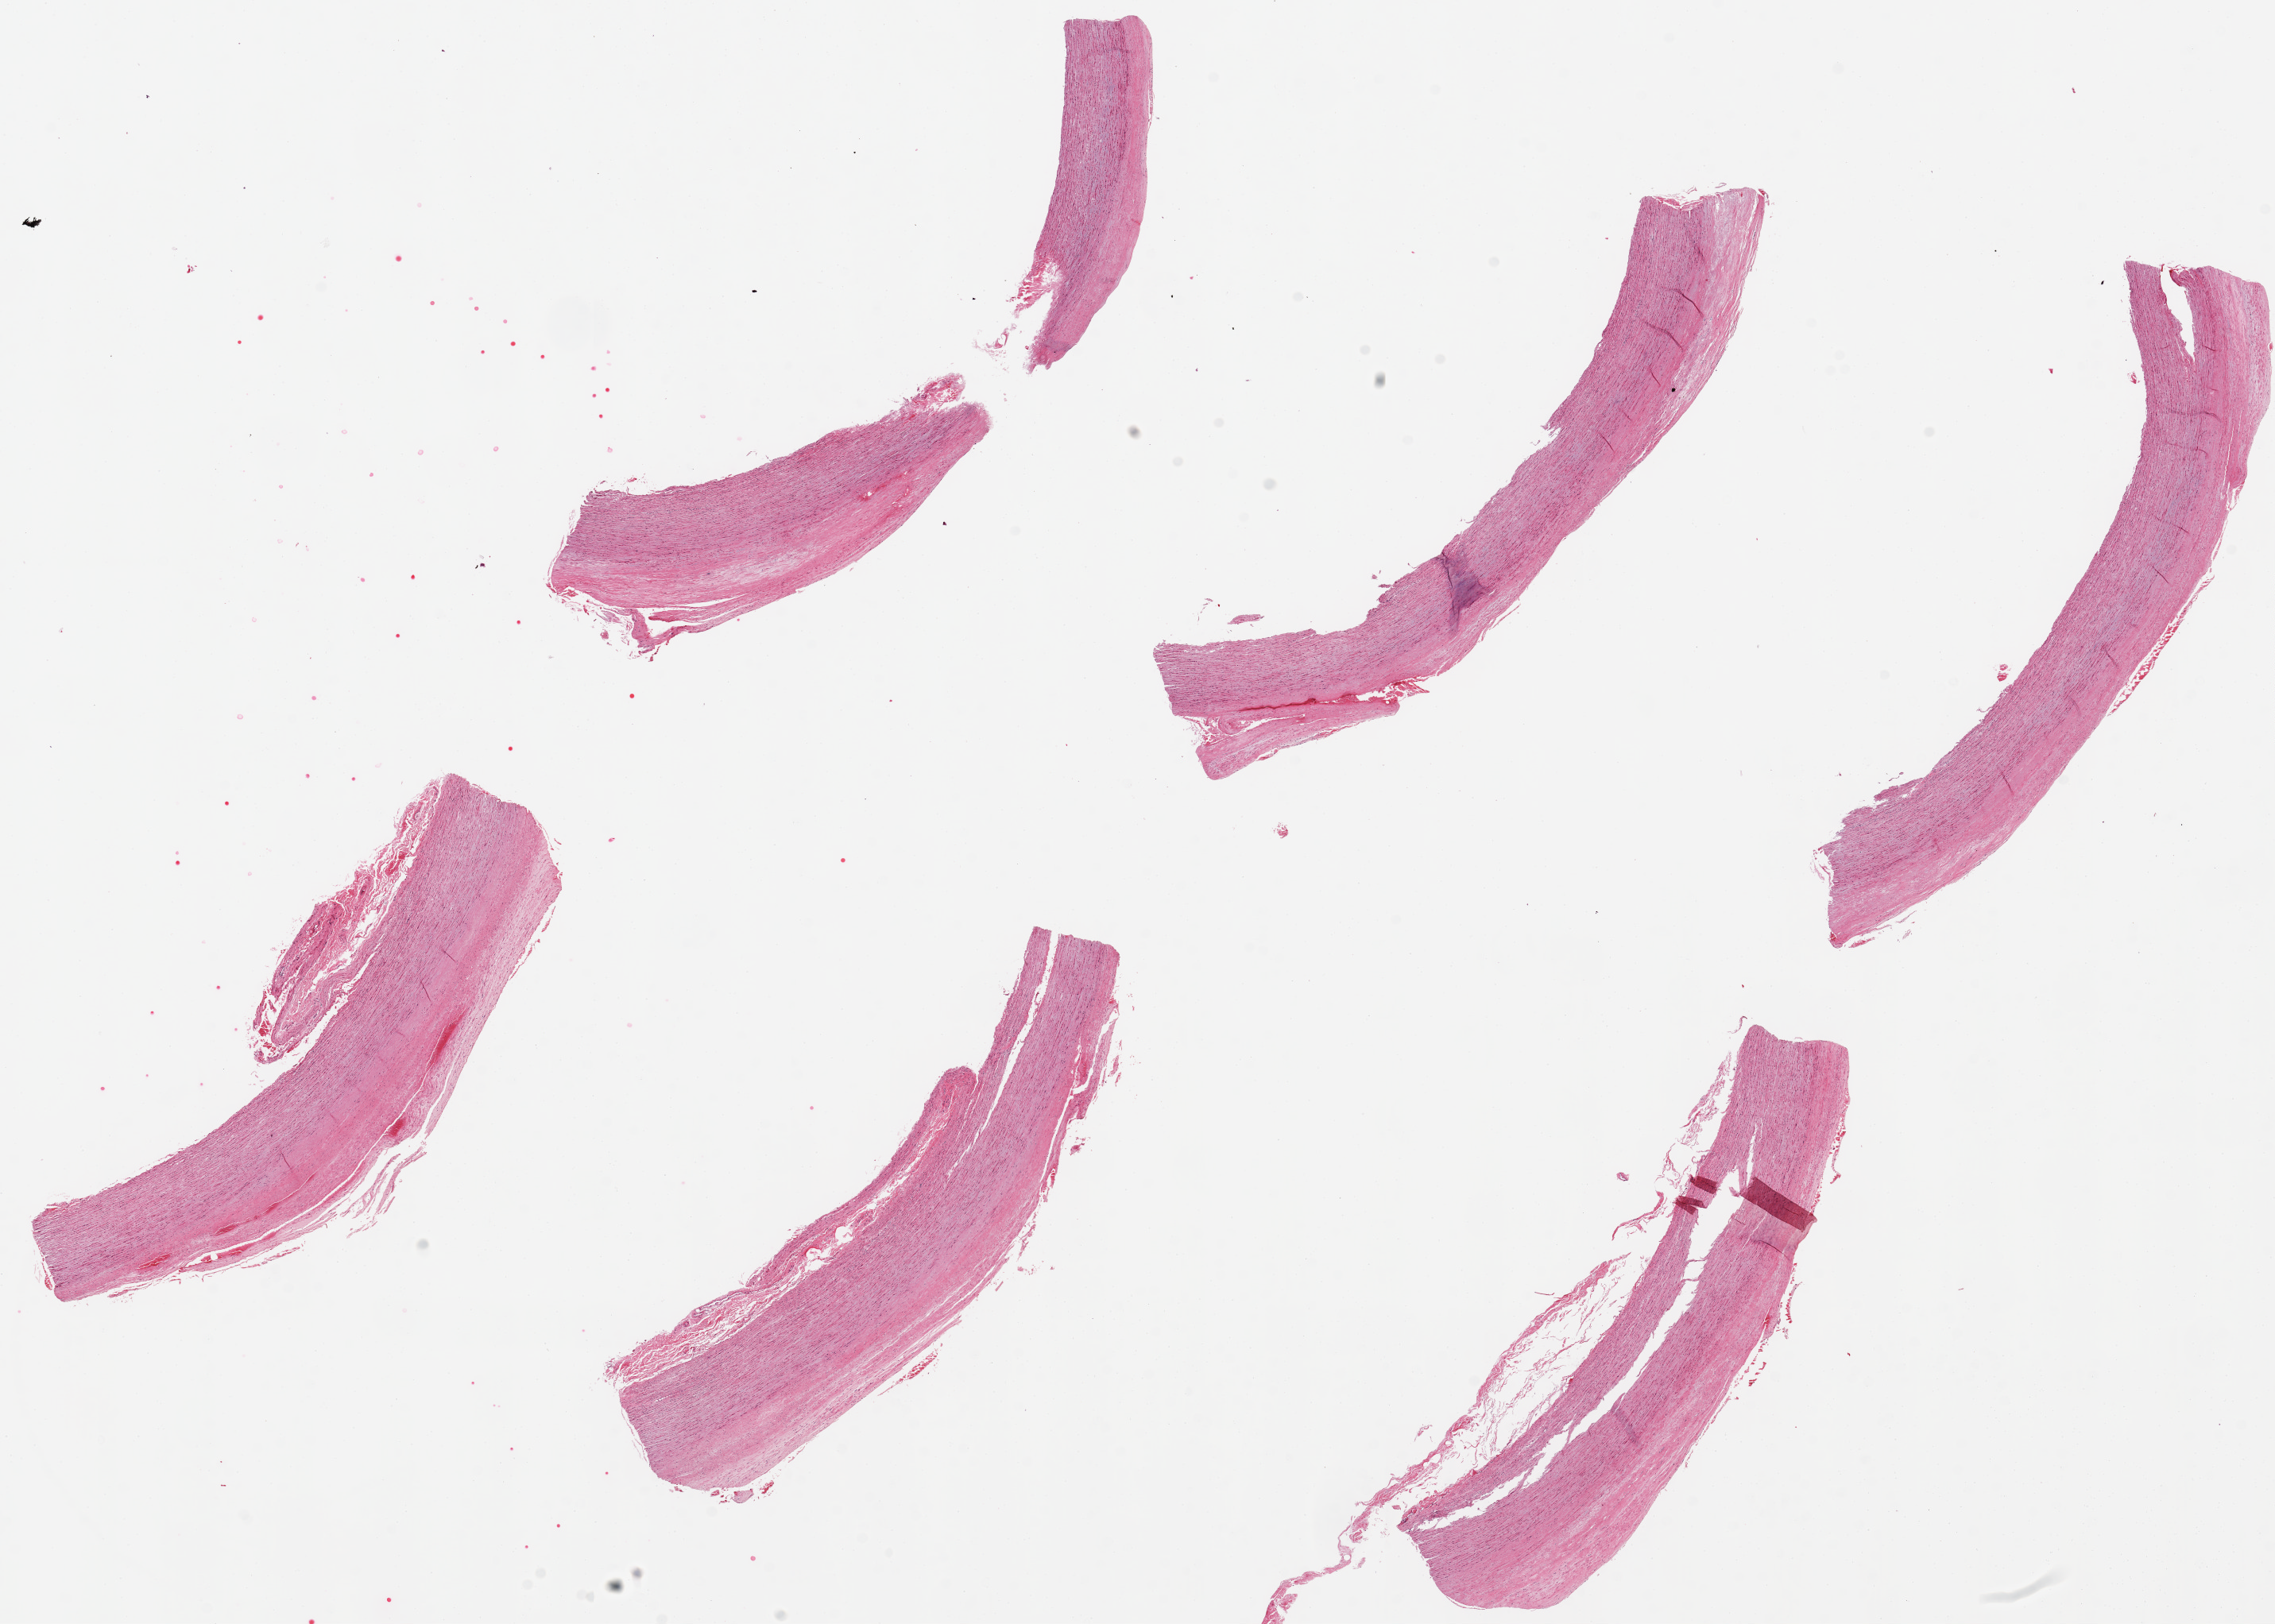
Haematoxylin and eosin whole-slide image, brightfield, whole scanned area (about 22.6 x 16.2 mm) shown as a low-resolution overview. PAXgene-fixed paraffin-embedded (PFPE) section. Target tissue: aorta. Donor tissue sample. Donor sex: female.
* pathologist's review note for this sample: 6 pieces. up to 8x2mm; Minimal periaortic stroma on 3 pieces. Flat plaques